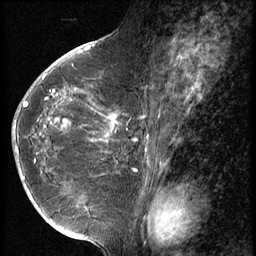
Breast MRI (dynamic contrast-enhanced), one sagittal slice. Slice 30 of 56 in the series (ordered by position). 3 images stored at this slice position (order not interpretable as contrast timing). 1.5 T. TE 4.2 ms, TR 9 ms. 2.5 mm slice thickness. 256 × 256 image matrix, field of view 180 × 180 mm. Patient: female, 49 years. From the clinical record (not read from this slice): setting: breast cancer imaged before/during neoadjuvant chemotherapy; receptor status: HER2-positive.
Outlined on this slice (semi-automatically segmented with operator editing):
- analysis volume of interest (the breast-tissue region the enhancement analysis was run in; not a lesion): box from (x=13, y=79) to (x=123, y=203) px
- tumour enhancement mask (voxels above the 140 % enhancement threshold inside the analysis volume of interest): (x=14, y=113)–(x=119, y=176)